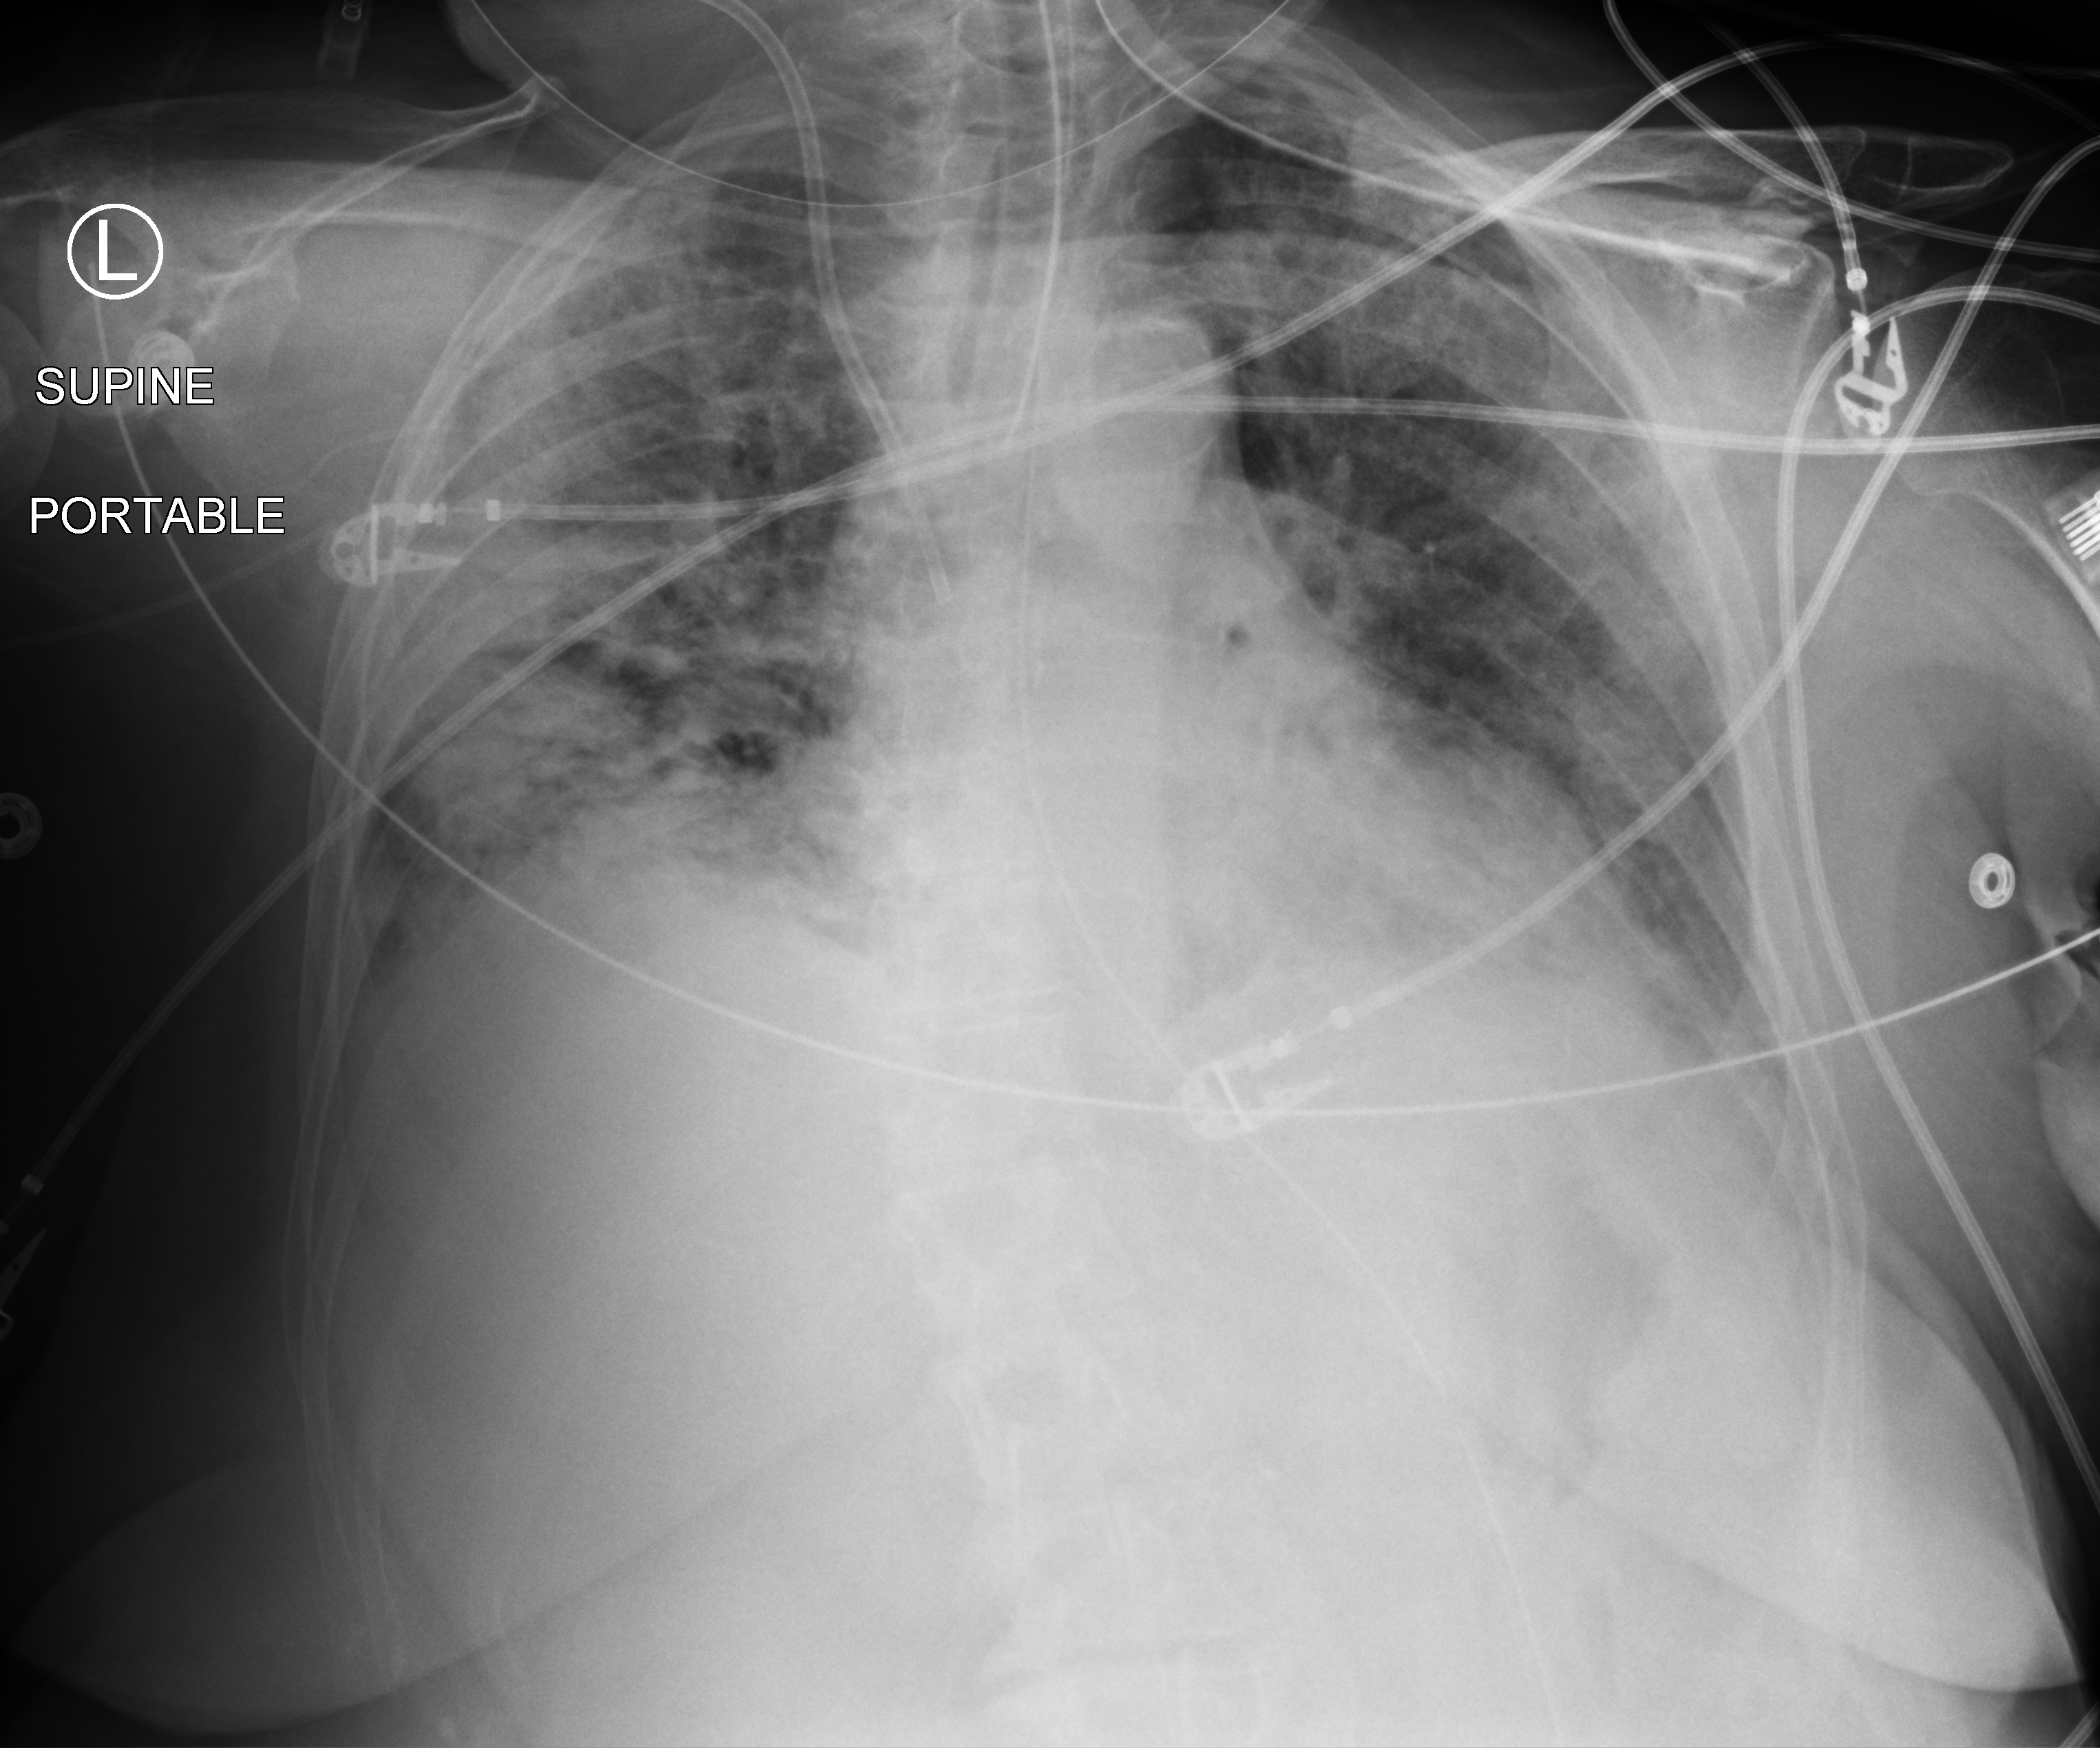
Bedside chest radiograph (computed radiography). Patient hospitalised with COVID-19; female, aged 75–90 years.
Admission-level facts for this patient (not findings on this image; timing relative to this image not recorded): mechanically ventilated during this hospital stay: yes.